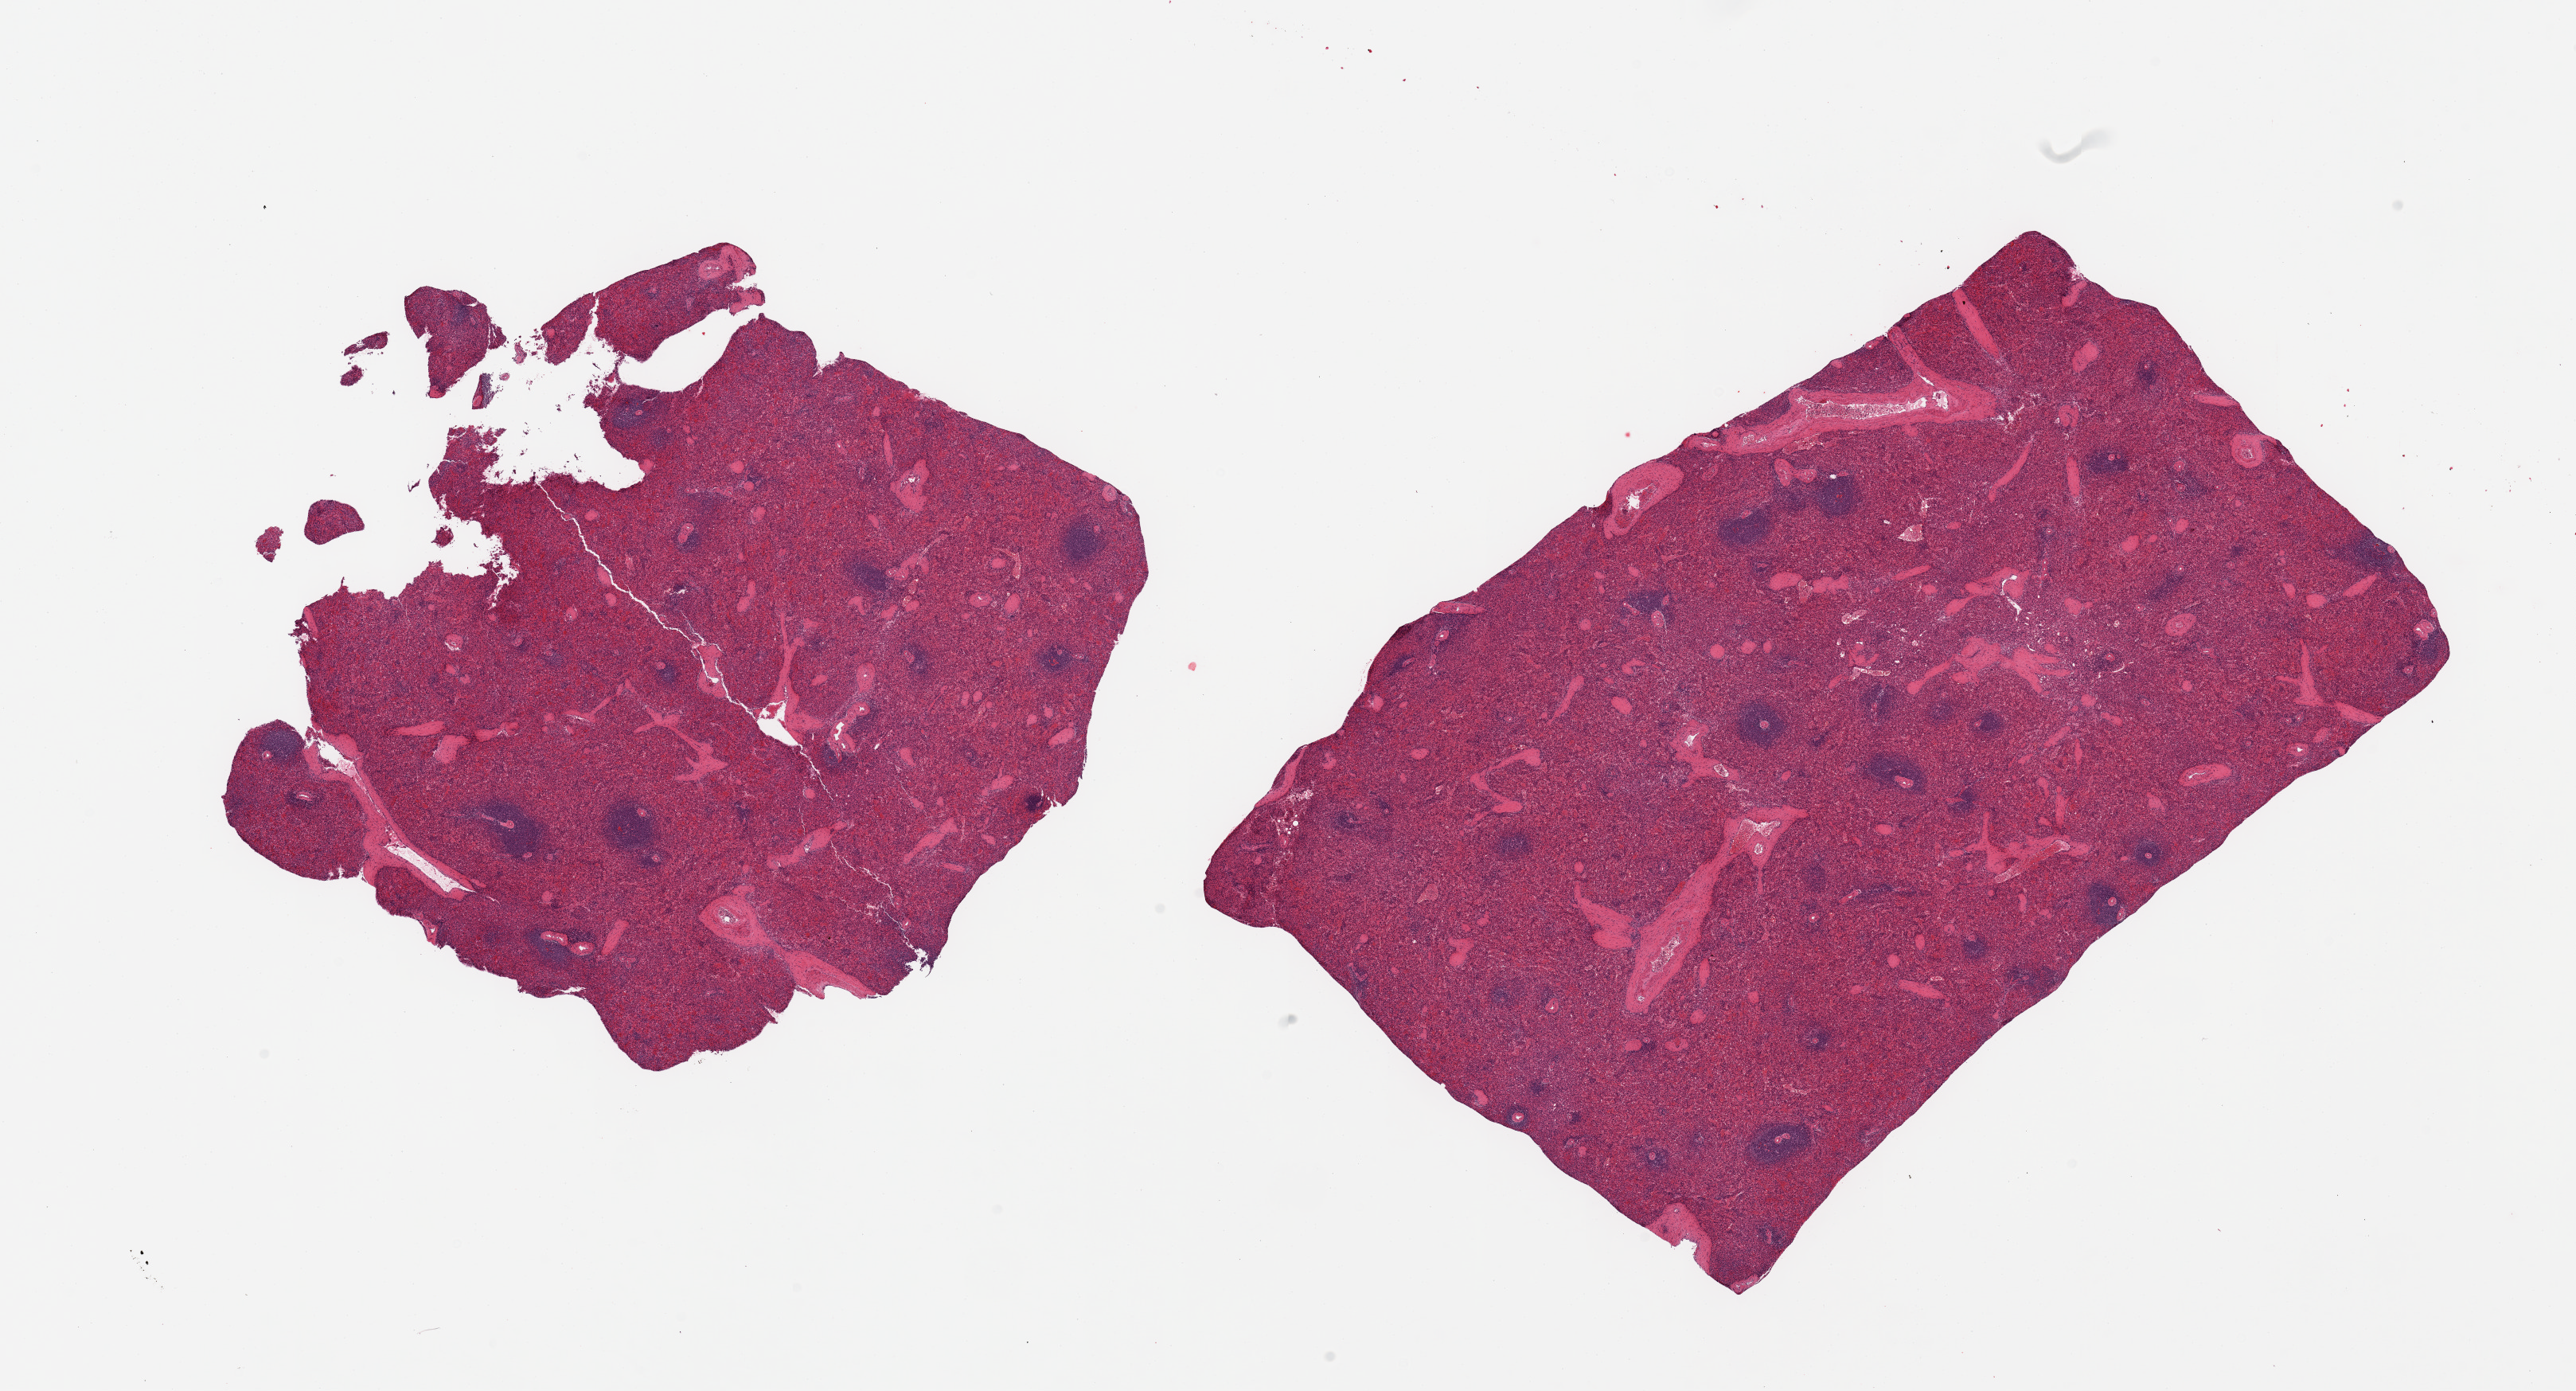
Digitized haematoxylin and eosin-stained section — shown as a low-resolution overview of the whole scanned area (about 25.6 x 13.8 mm); PAXgene-fixed paraffin-embedded (PFPE) section; section of spleen (target tissue); donor tissue sample. Male donor.
- pathologist's review note for this sample: 2 pieces, no abnormalities